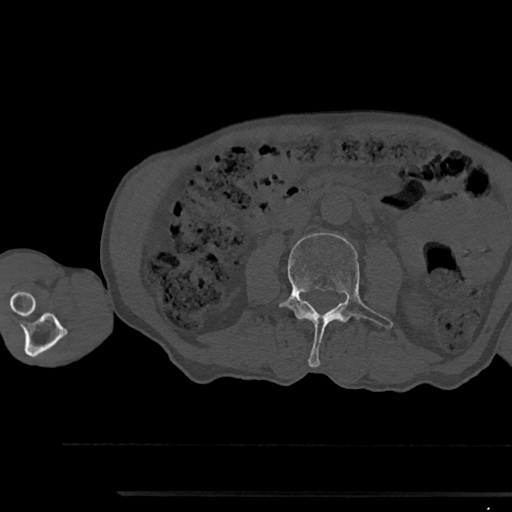
CT including the spine, one axial slice; slice 491 of 797 in the series (ordered by position); reconstruction kernel Br40s/3; 120 kVp; bone window (W 1800 / L 400 HU); 512 × 512 image matrix, field of view 367 × 367 mm. Patient: male, 79 years. From the clinical record (not read from this slice): primary cancer: prostate.
Structures marked on this image (semi-automatically segmented with operator editing):
- L3 vertebra: bounding box [x1, y1, x2, y2] px = [280, 233, 393, 367]